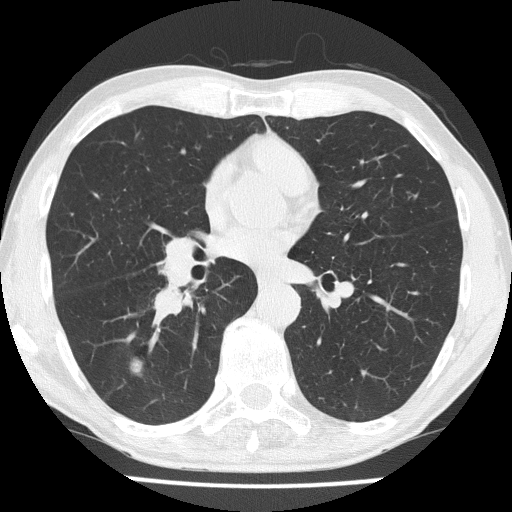
Low-dose screening chest CT, axial slice; third screening round (two years after baseline); lung window (W 1500 / L -600 HU); 2 mm slice thickness; 120 kVp. Male participant, aged 59 years at enrolment. Former smoker at enrolment.
Lesion marked by an expert reader, bounding box [x1, y1, x2, y2] px = [113, 345, 157, 390]. Screening reader's record for this exam (one nodule recorded; not confirmed to be the boxed lesion): non-calcified nodule or mass ≥4 mm, right lower lobe, 20 × 16 mm, smooth margins, soft tissue attenuation, pre-existing on the prior screen: no. Participant outcome: lung cancer diagnosed 25 days after this screen — small cell carcinoma, NOS, right lower lobe, stage IIA (AJCC 6th edition), 20 mm at pathology.